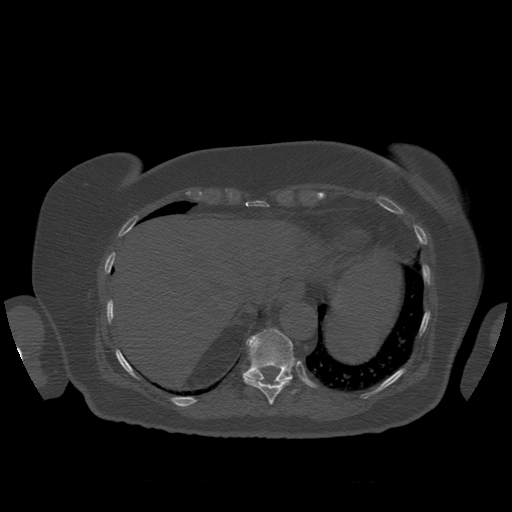
CT including the spine, one axial slice. Slice 332 of 399 in the series (ordered by position). Reconstruction kernel STANDARD. Bone window (W 1800 / L 400 HU). 512 × 512 image matrix. Patient age 81 years. From the clinical record (not read from this slice): primary cancer: renal.
Annotated regions visible in this slice (semi-automatically segmented with operator editing):
- T10 vertebra: bounding box (x1, y1, x2, y2) in pixels: (243, 376, 293, 405)
- T11 vertebra: (243, 328, 299, 394)